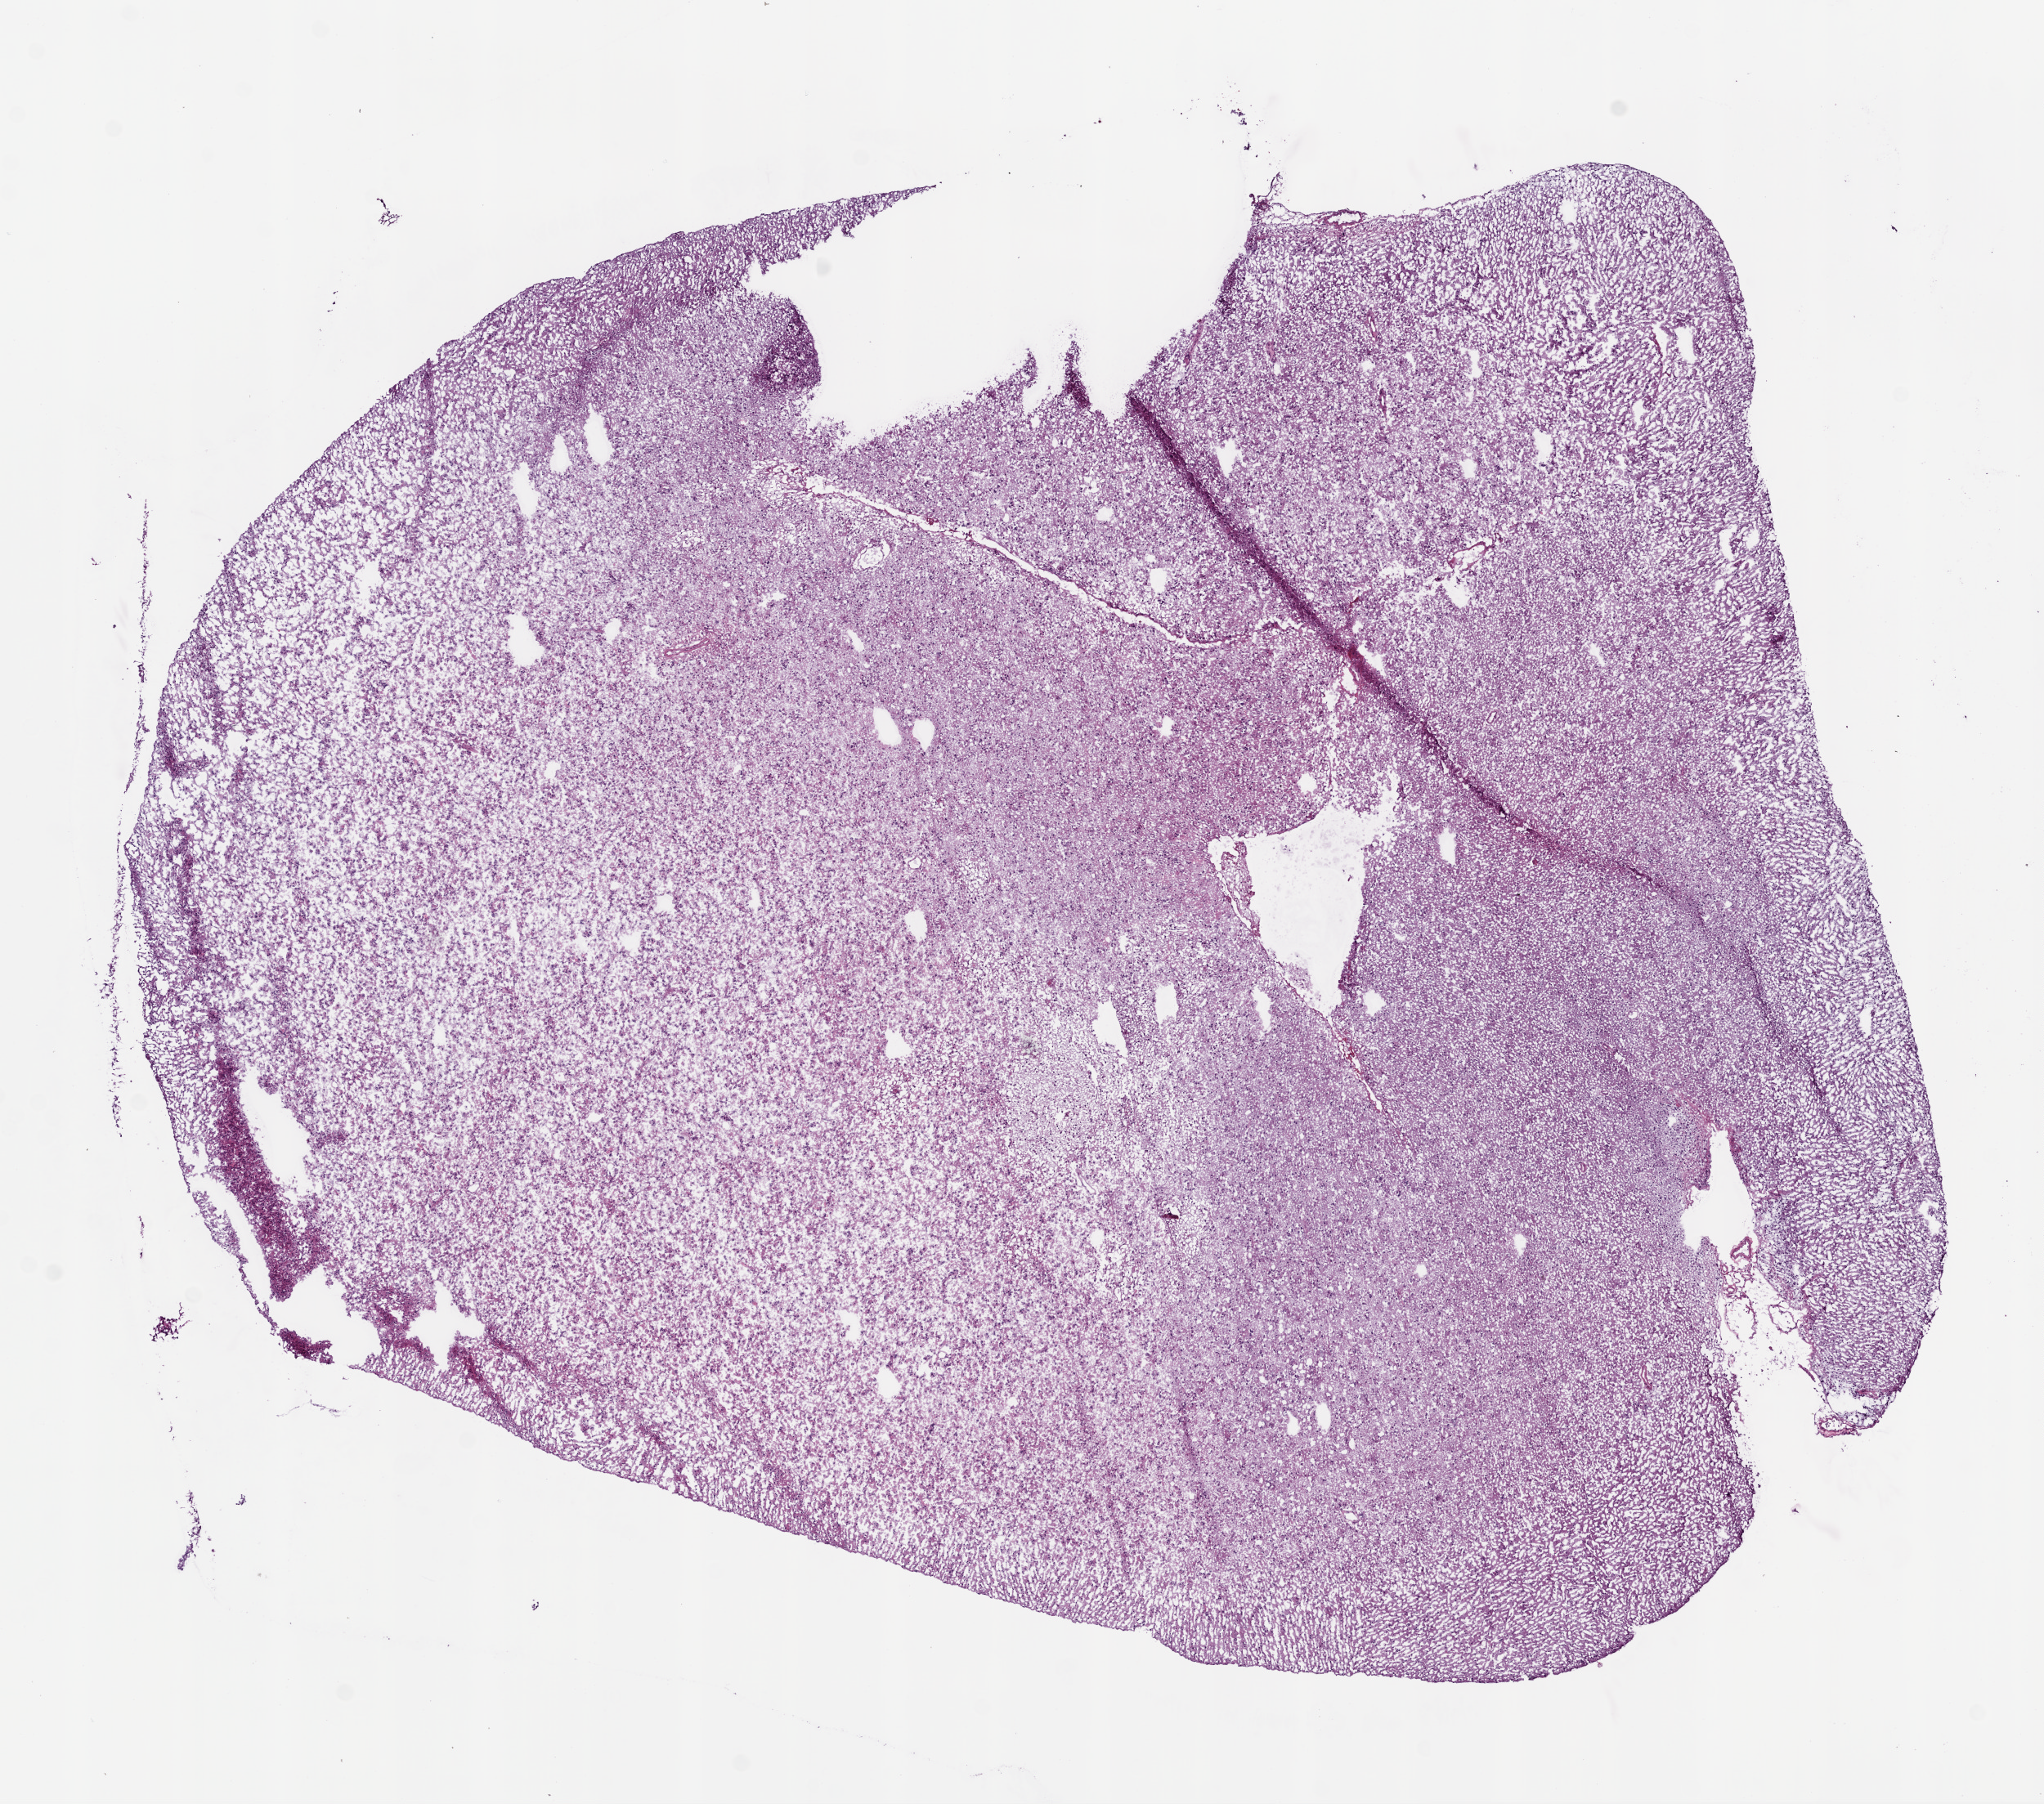
Hematoxylin and eosin (H&E) stained whole-slide image, whole scanned area (about 10.0 x 8.9 mm) shown as a low-resolution overview; frozen section; primary tumour sample from the brain. Patient: male, age at initial diagnosis 34 years. Histologic grade: G3 (poorly differentiated). Composition of this section per pathologist review: tumour cells 100%, tumour nuclei 65%, normal cells 0%, stromal cells 0%, necrosis 0%.
Pathologic diagnosis: Astrocytoma, anaplastic. Laterality: right.